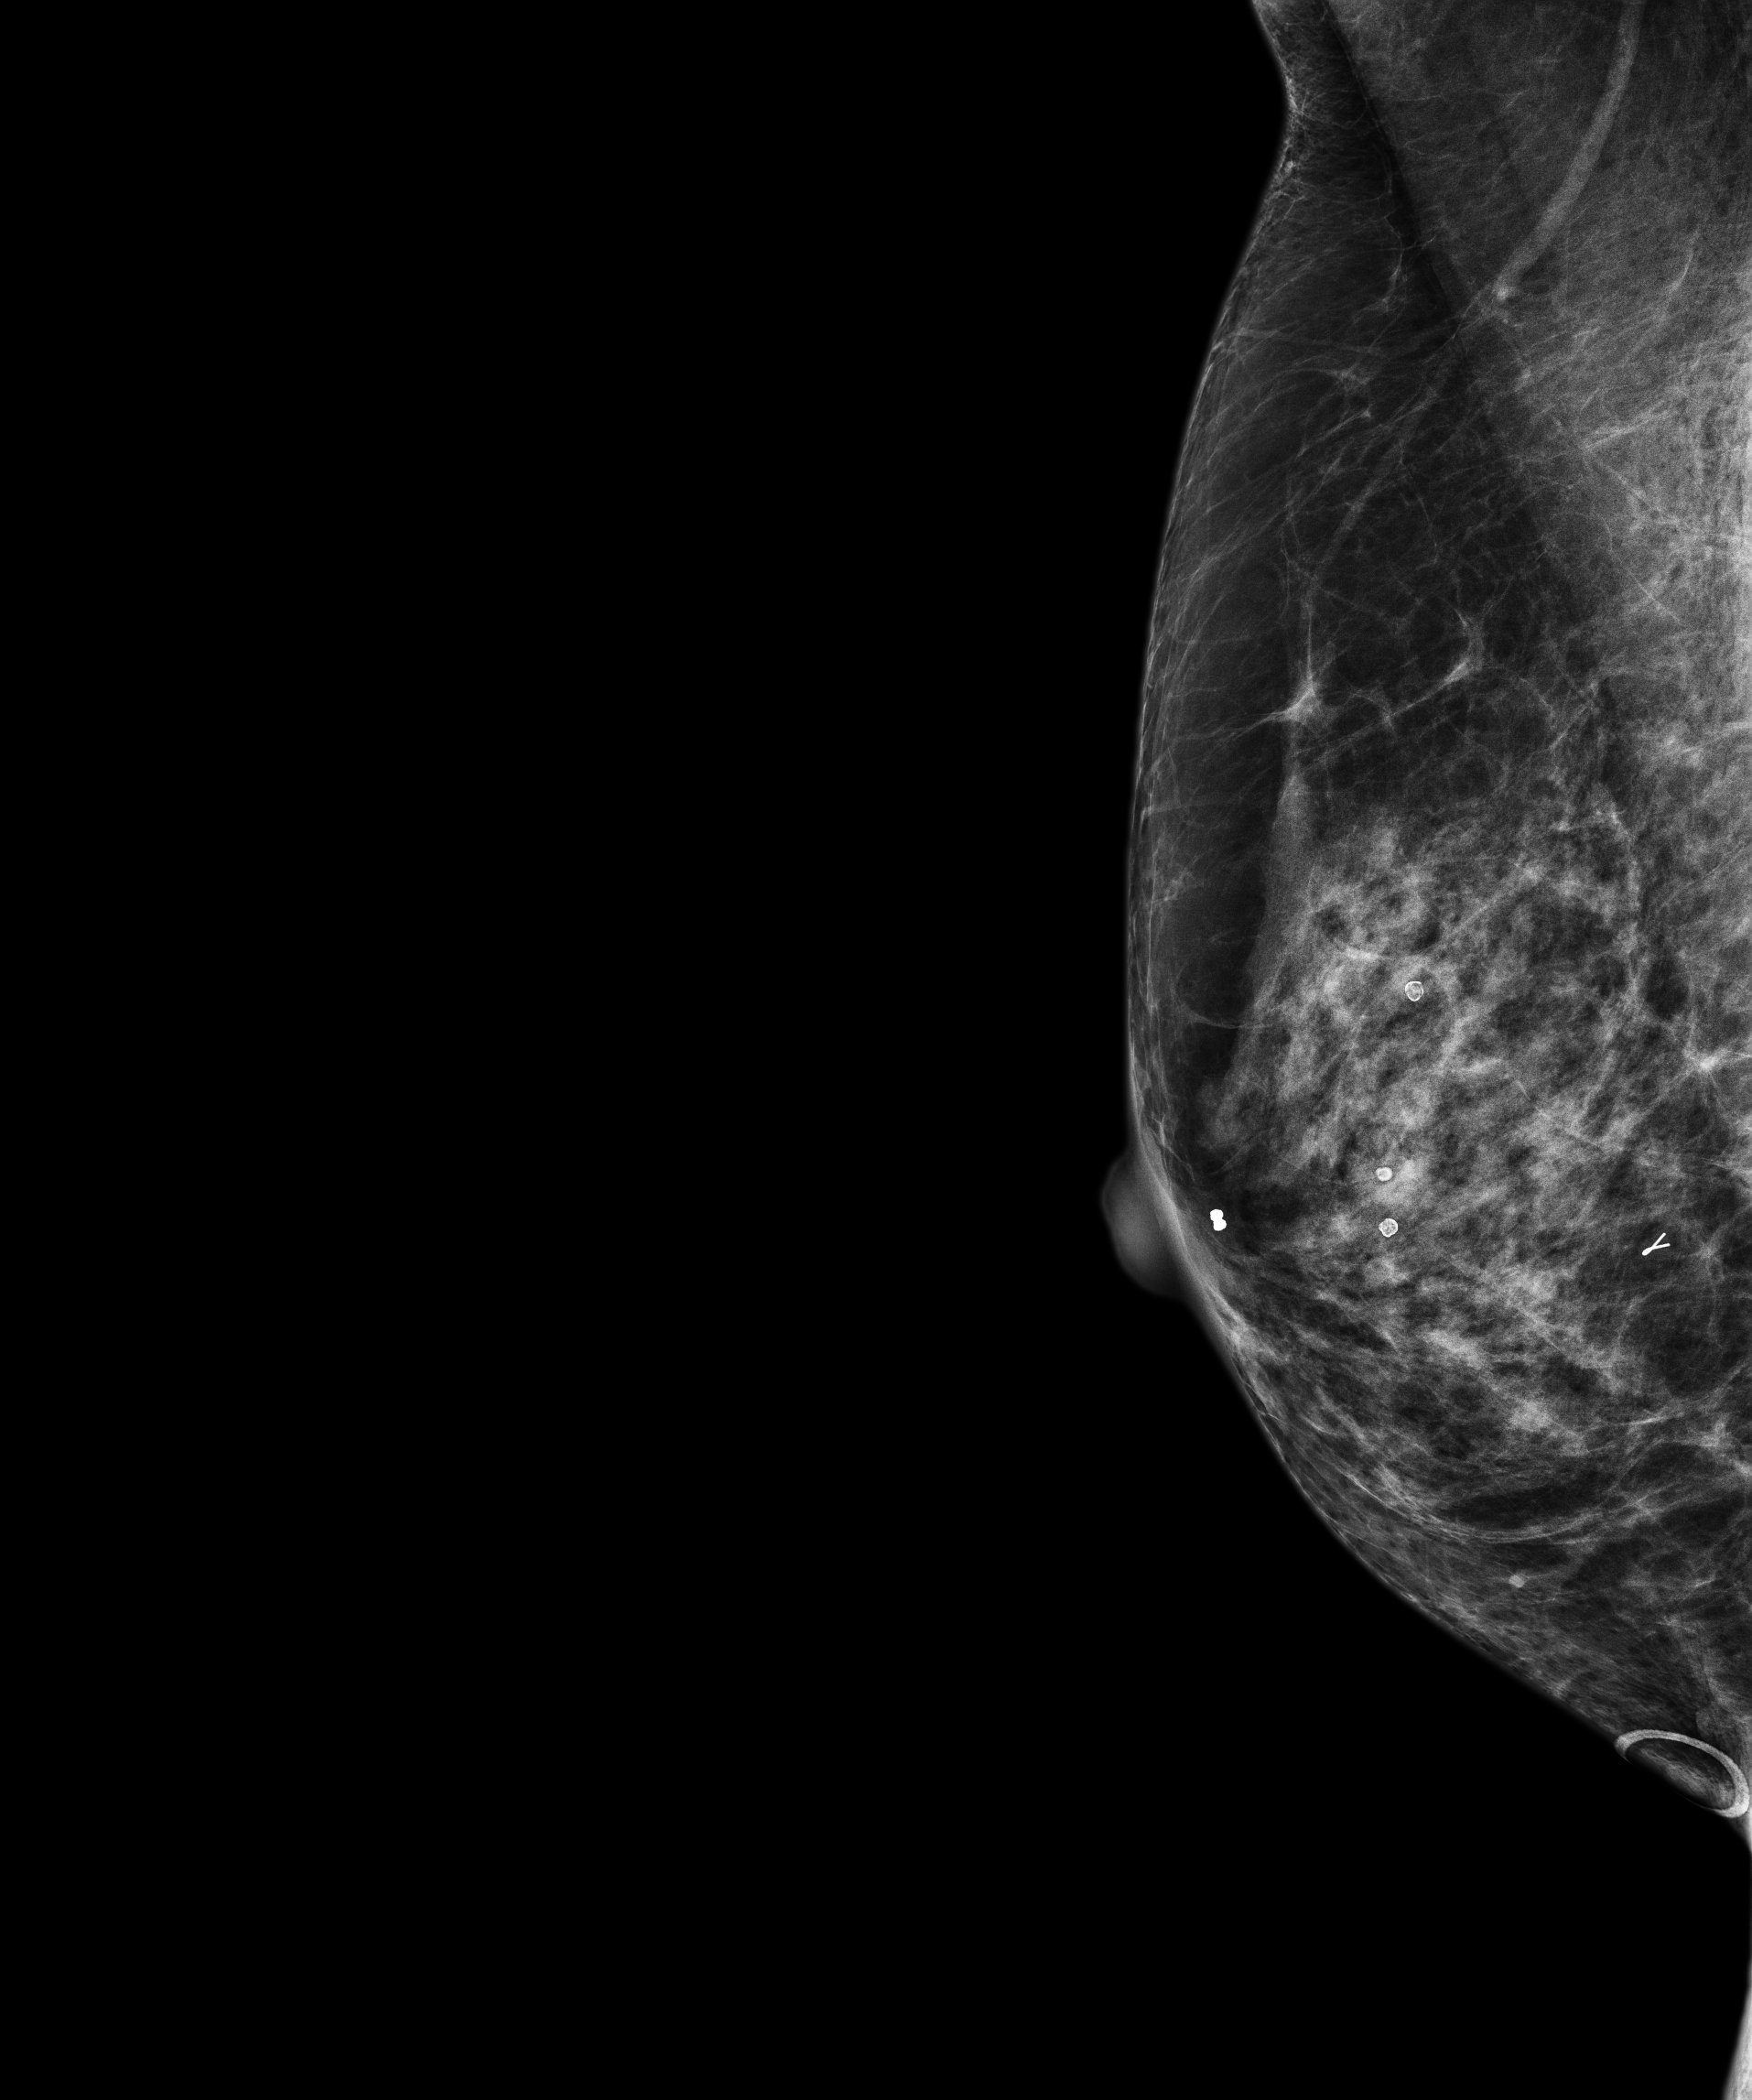
Annual screening mammography examination, compressed breast thickness 51.1 mm, system: Senographe Pristina. Patient aged 65 years (female).
Image type: full-field digital mammogram. Breast: right. Projection: MLO view.